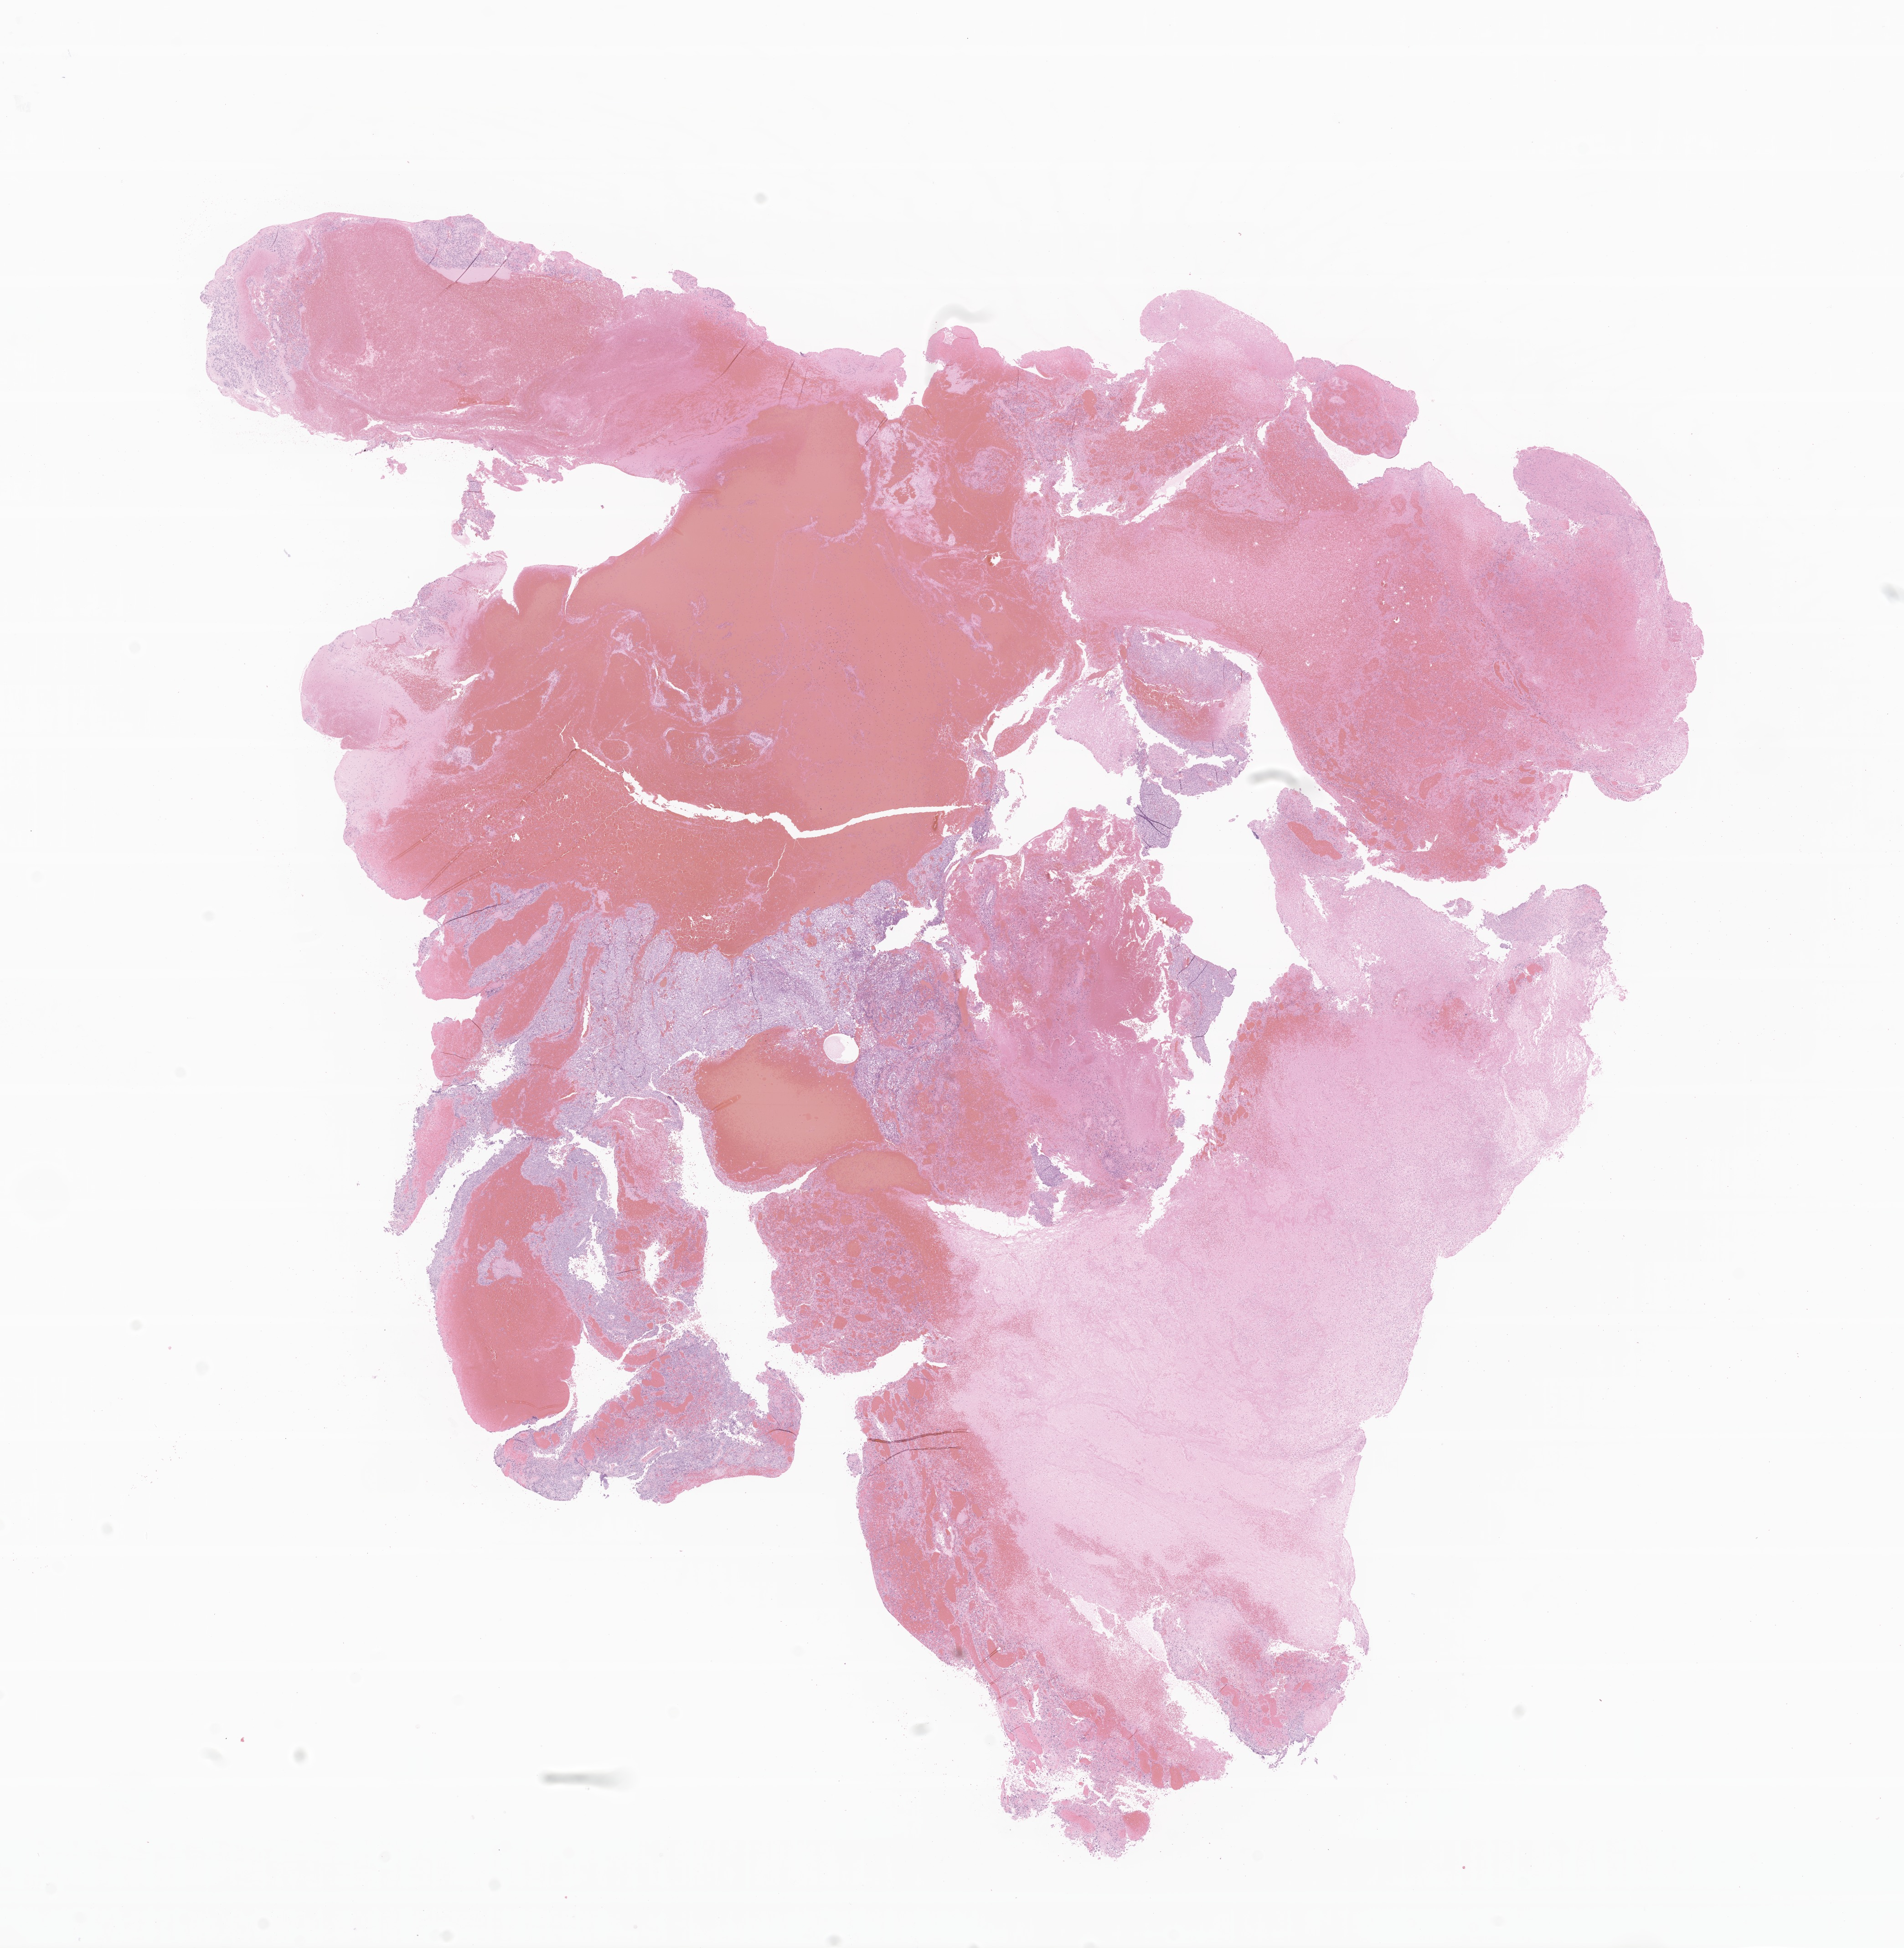
Whole-slide image, hematoxylin and eosin (H&E) stain of tumor tissue from the temporal lobe — whole scanned area (about 17.6 x 18.0 mm) shown as a low-resolution overview; formalin-fixed paraffin-embedded section. Patient: male, age 214 months (17 years 10 months).
- diagnosis (ICD-O-3 morphology term): Gliosarcoma